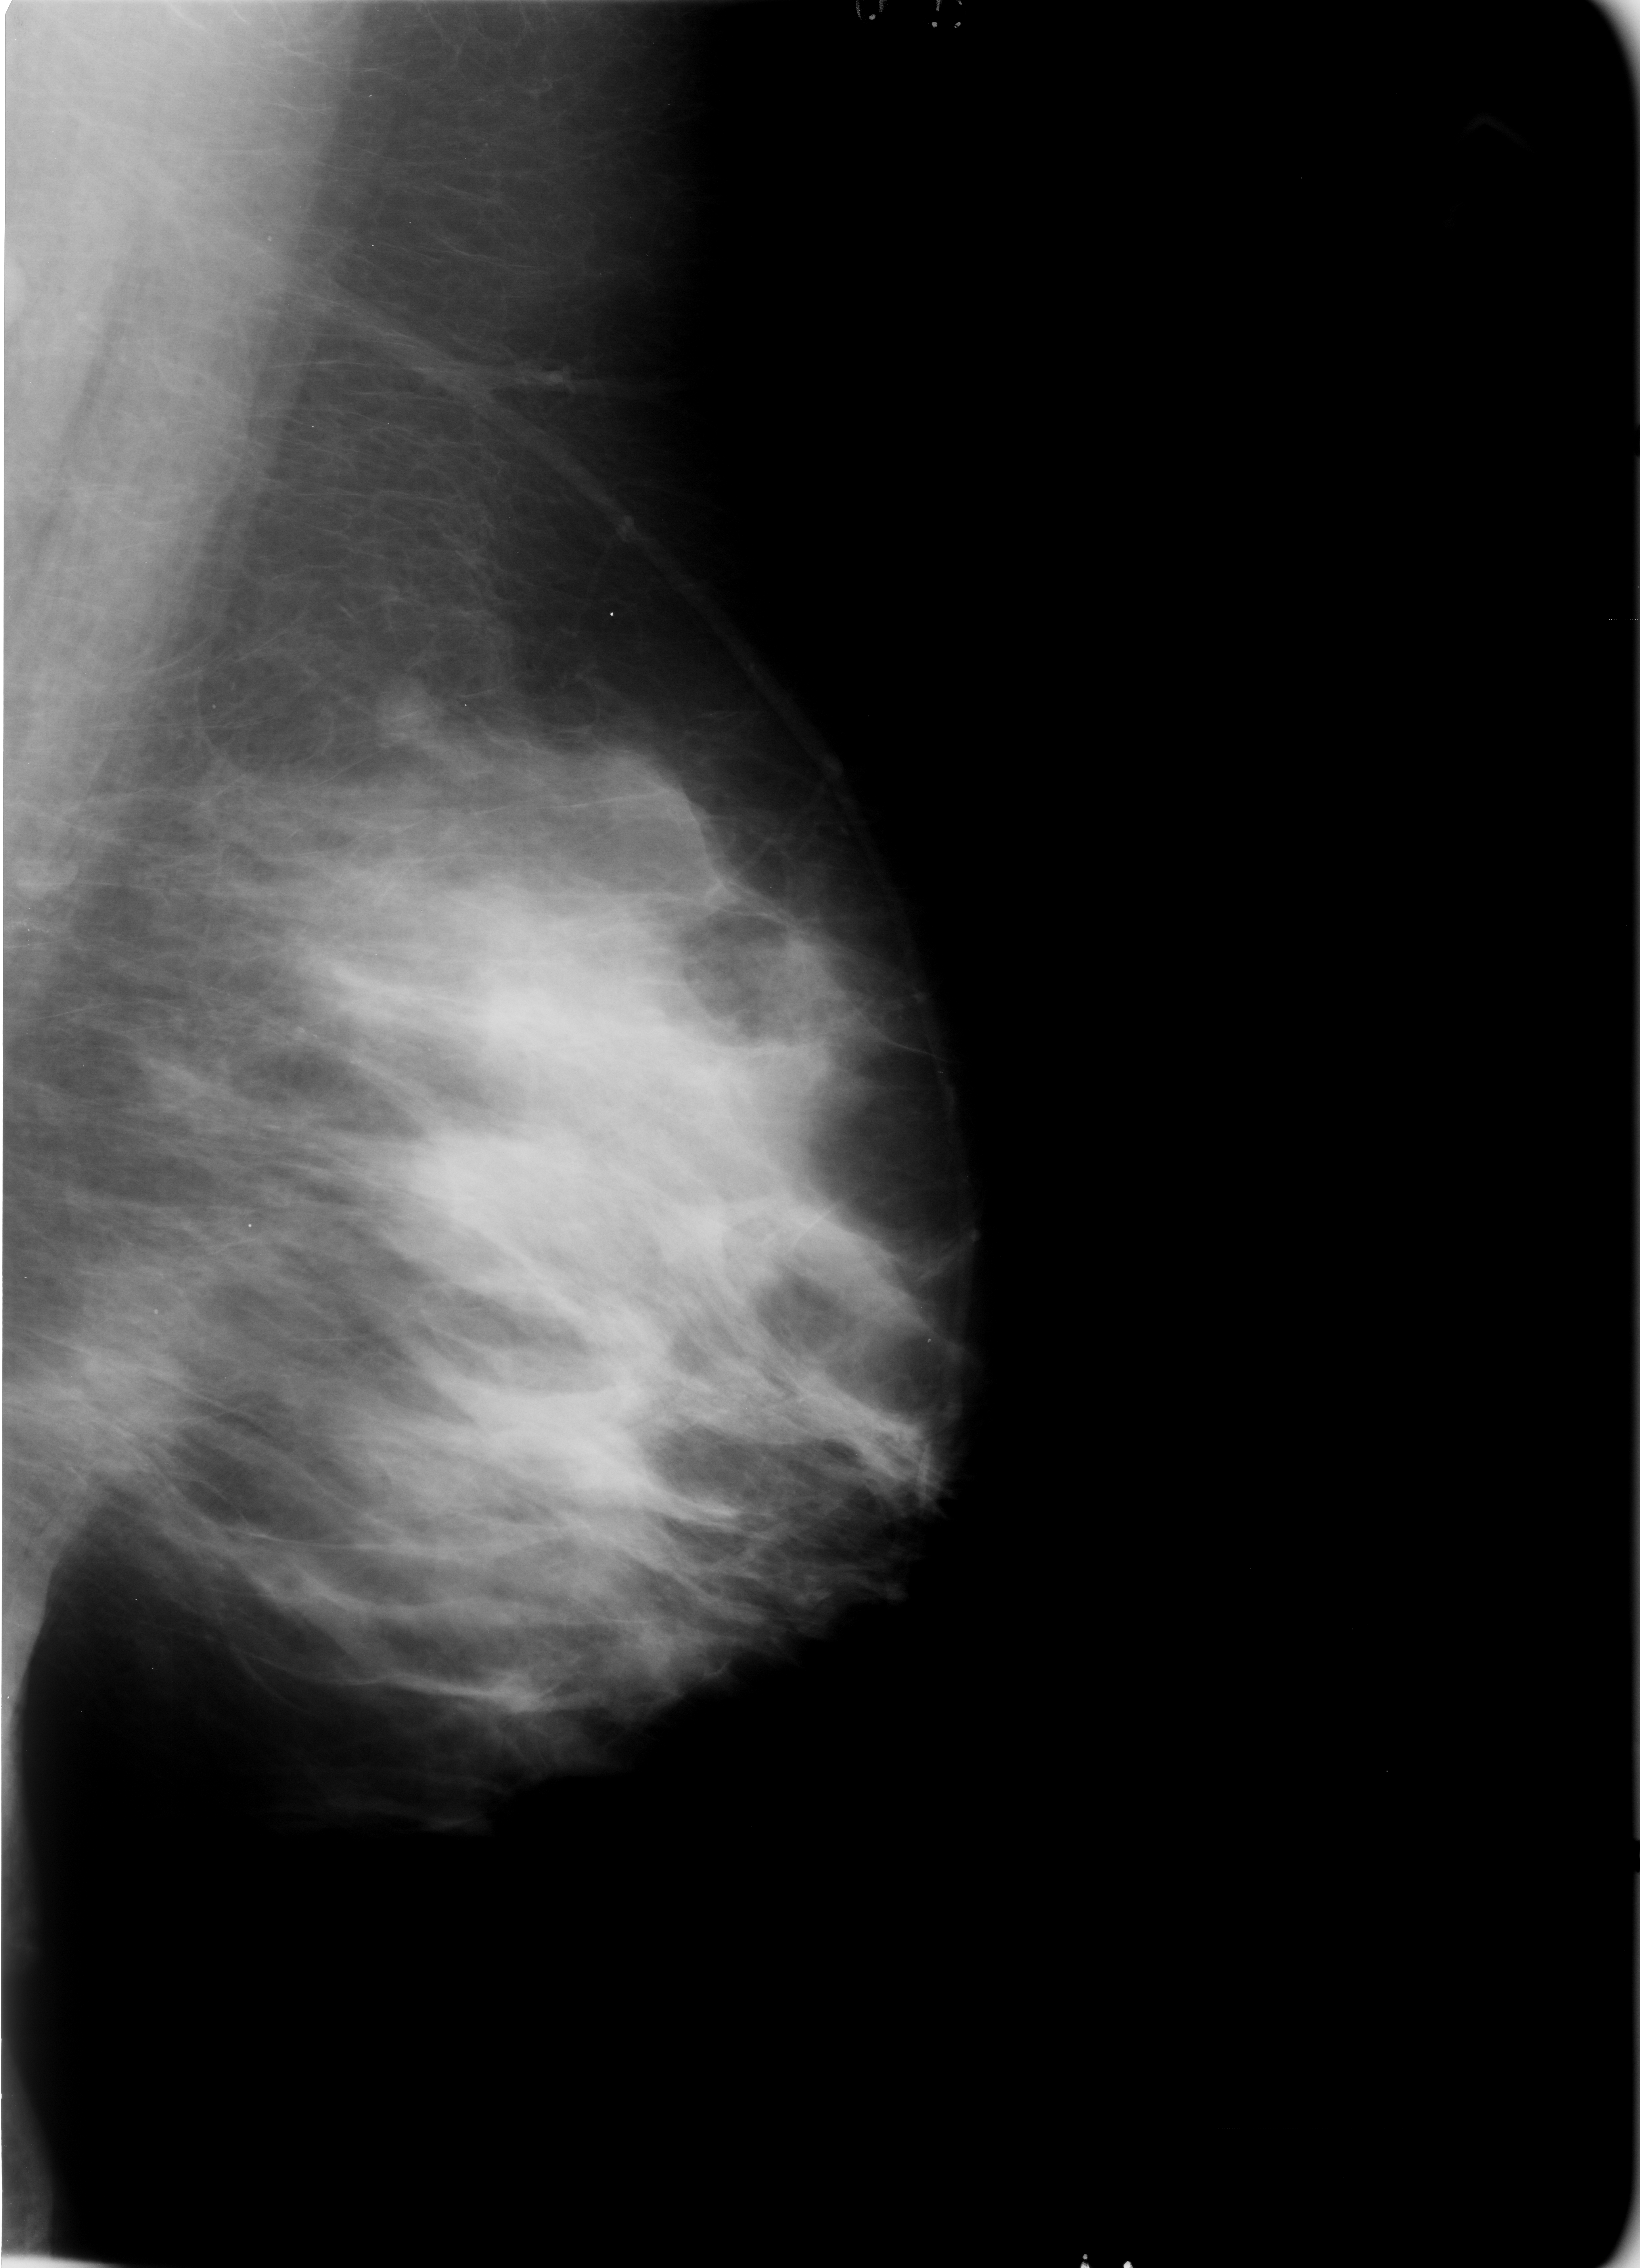
Digitized screen-film mammogram; left breast; MLO view; BI-RADS breast density category 3 (scale 1–4); 1640 × 2268 image matrix.
Expert-marked regions of interest on this film, with their recorded descriptors:
- calcifications, morphology vascular; BI-RADS assessment category 2; subtlety rating 3 on a 1 (subtle) to 5 (obvious) scale; benign; no additional work-up was recommended (outcome (as recorded, no biopsy): benign without callback): bounding box [x1, y1, x2, y2] px = [0, 793, 334, 921]